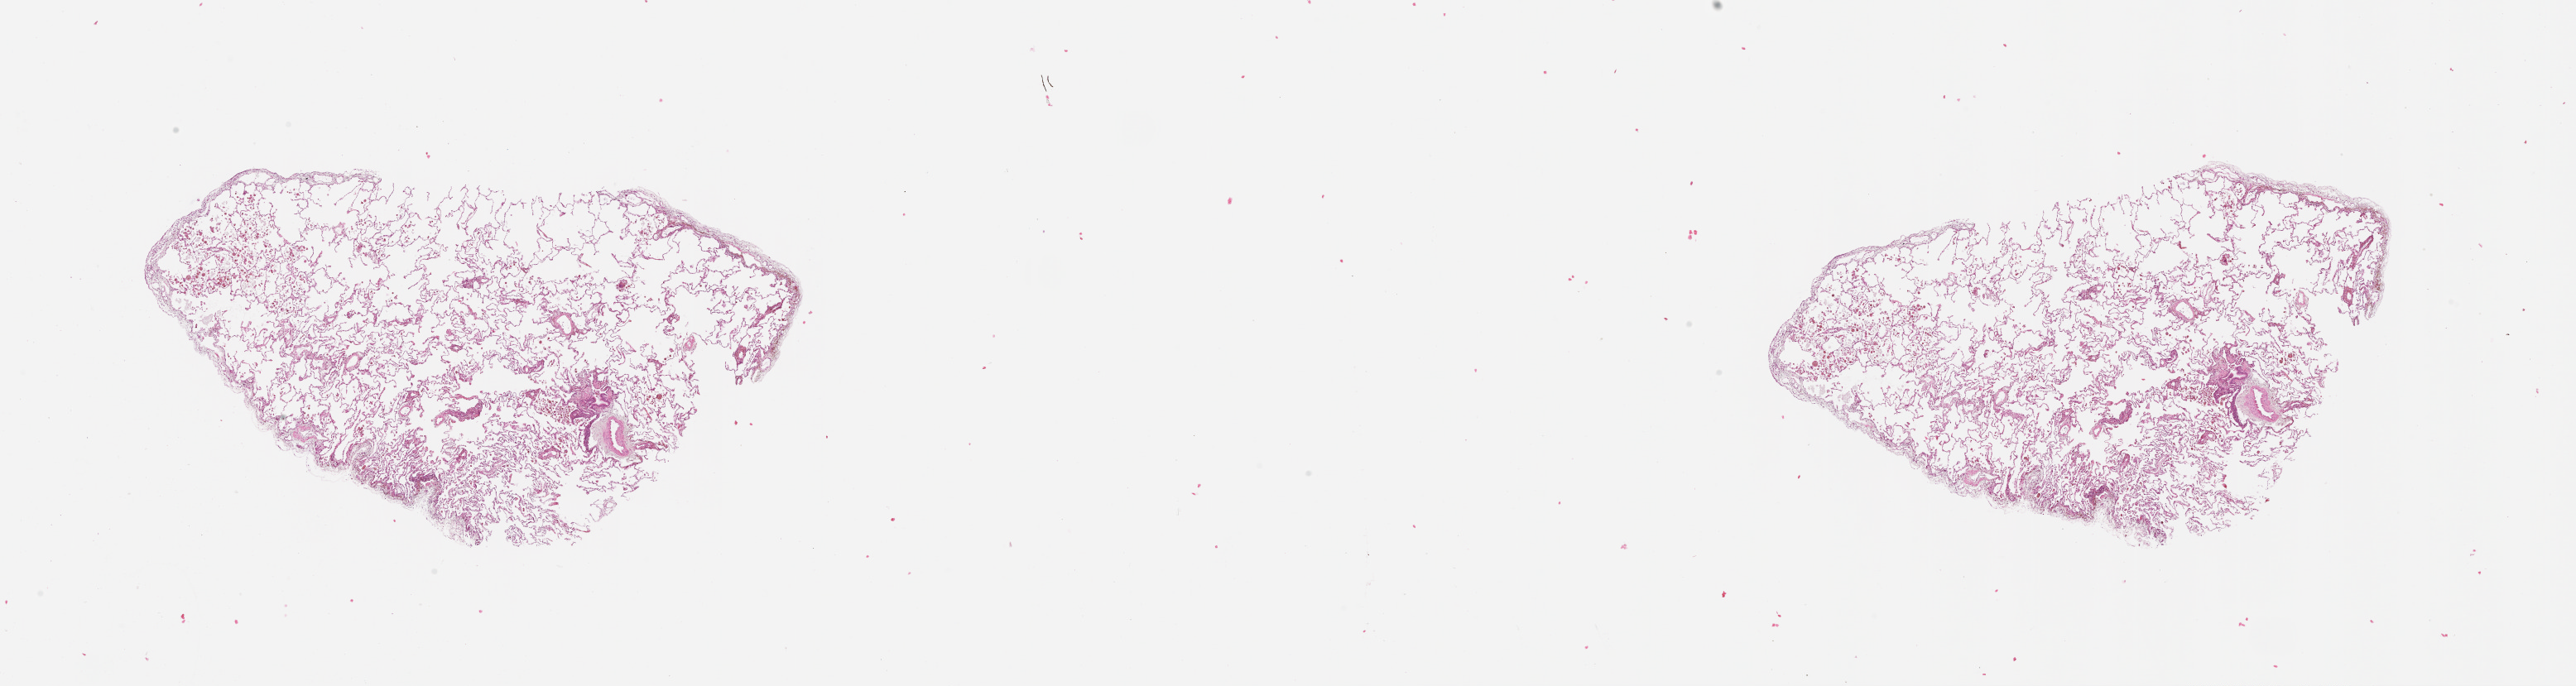
Digitized Hematoxylin and eosin (H&E) stained tissue section (whole slide) — shown as a low-resolution overview of the whole scanned area (about 25.1 x 6.7 mm, slide scanned at 20x). Lung, tissue type not recorded.
* patient diagnosis (cohort enrolment): lung adenocarcinoma (lung)